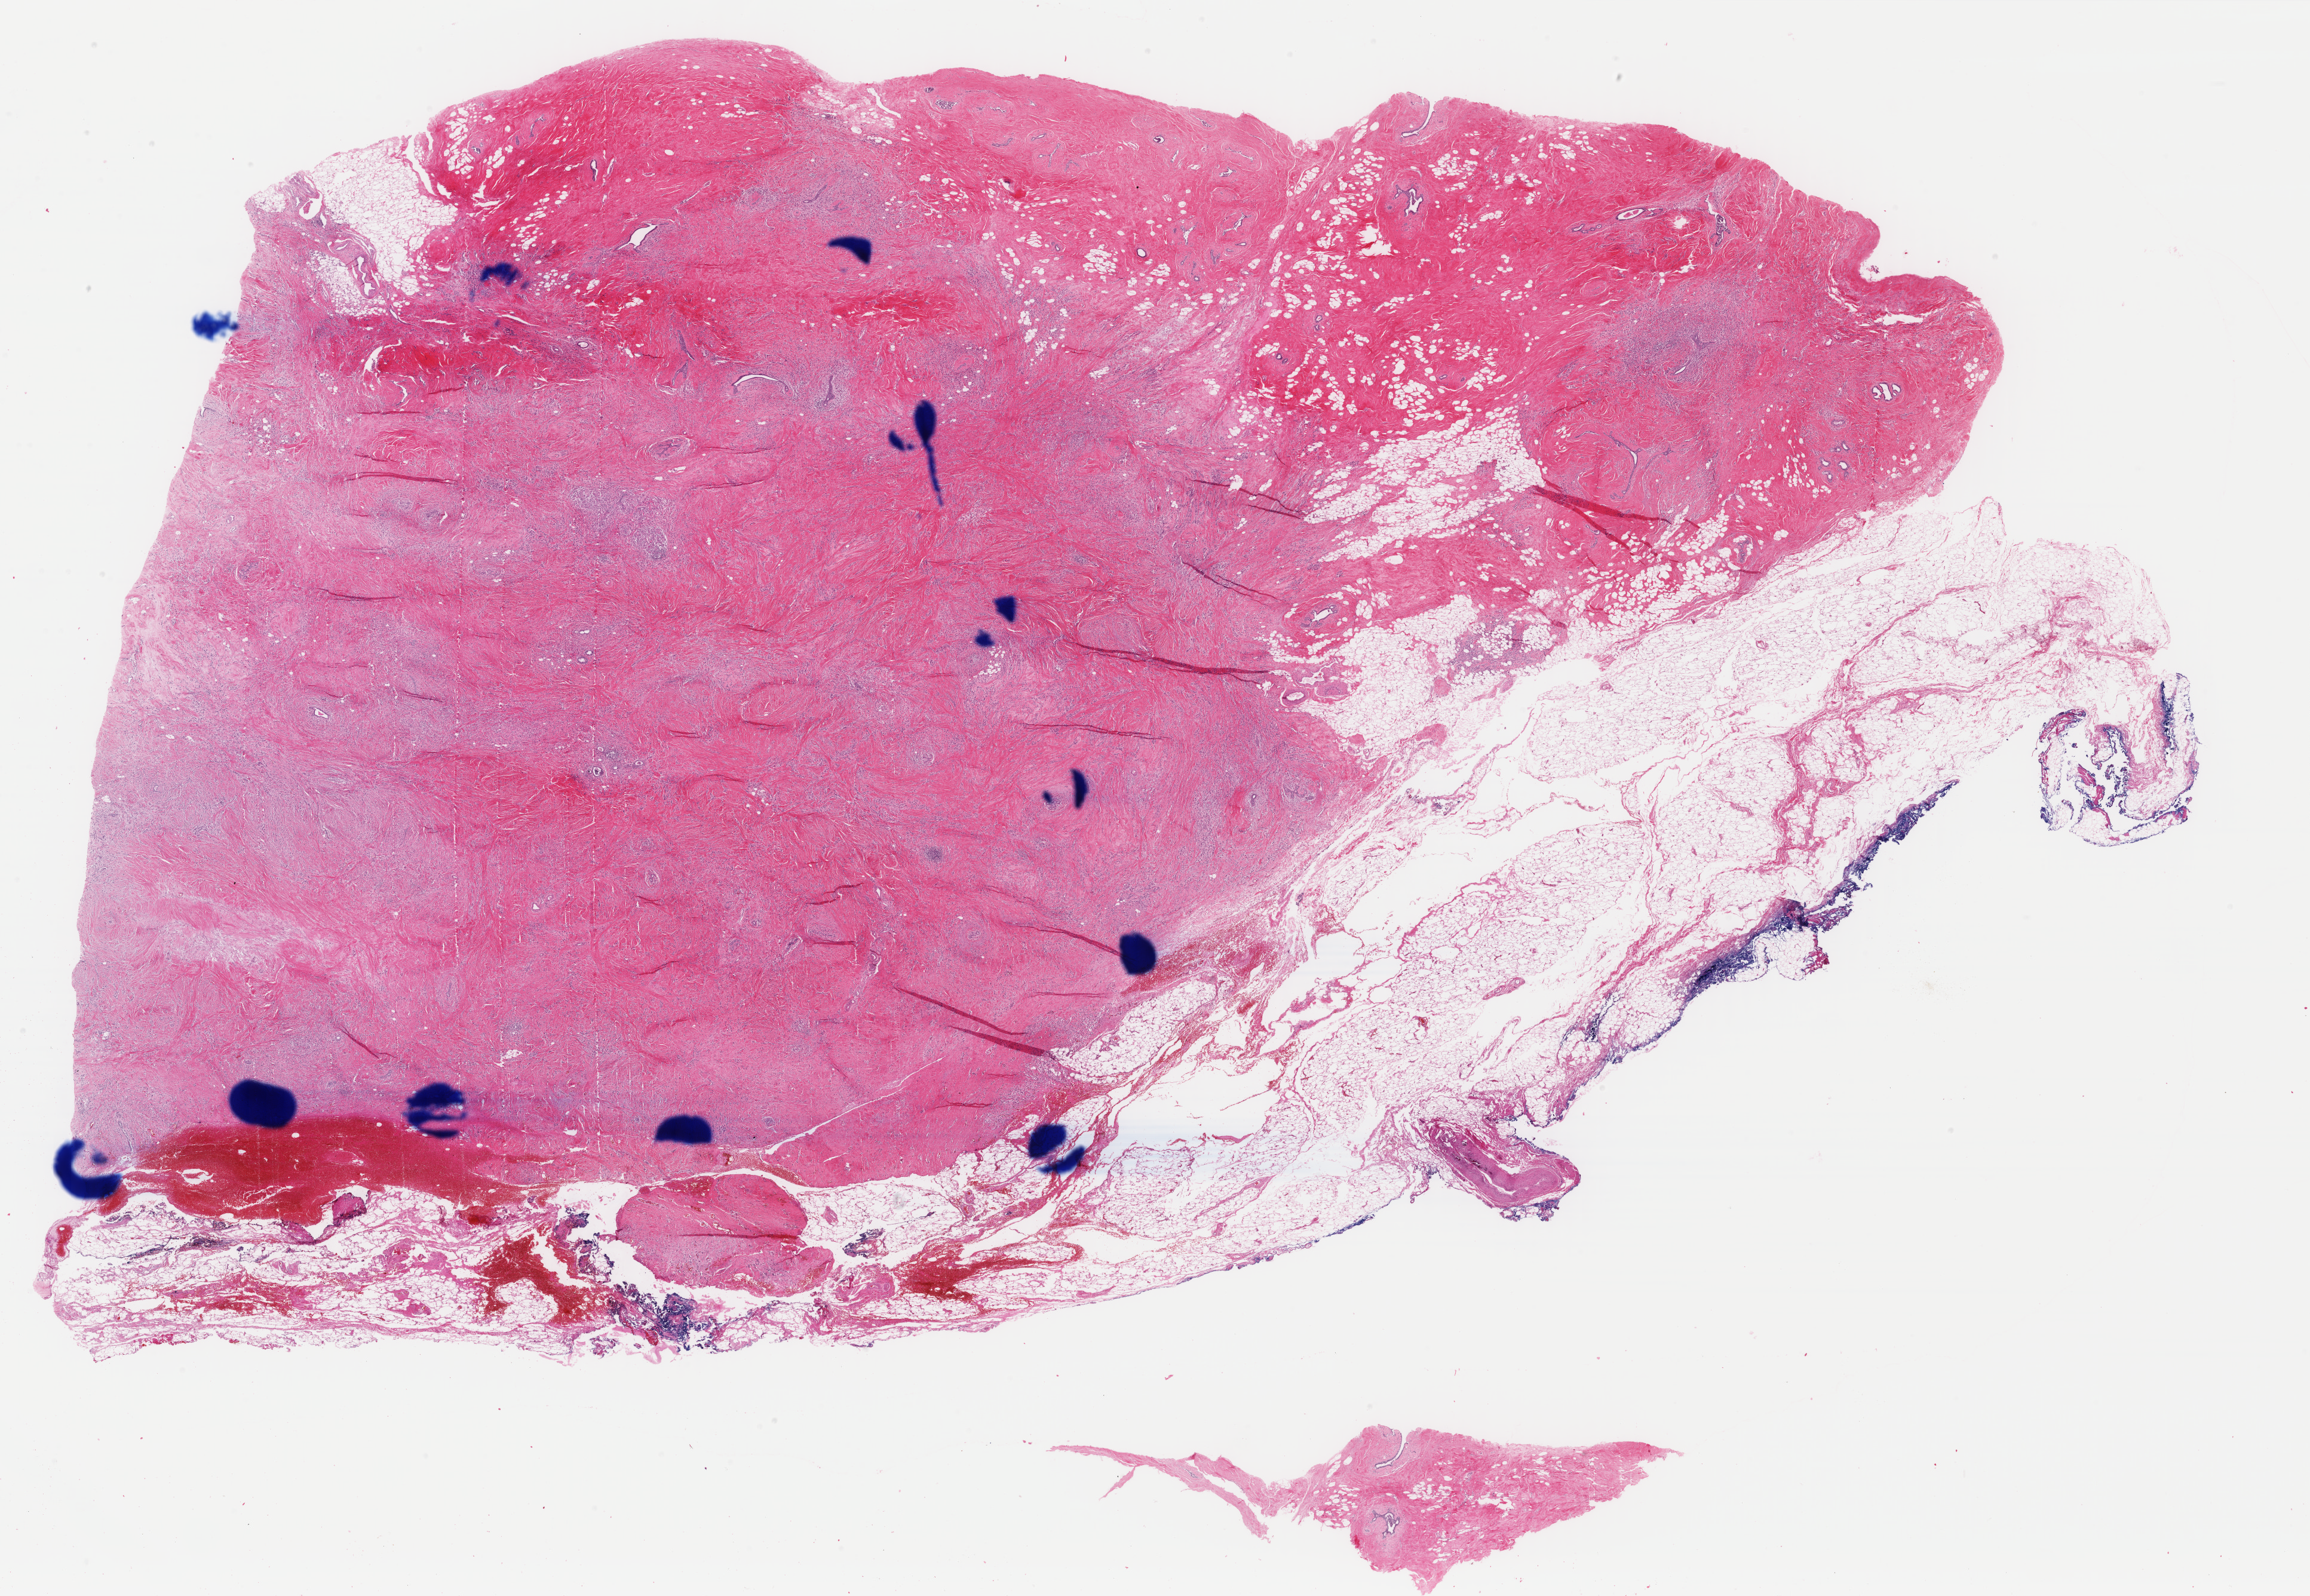
Whole-slide histology image, H&E-stained, low-resolution overview of the scanned area, about 30.7 x 21.2 mm (from a 40x scan). FFPE section. Primary tumour sample from the breast. Female patient.
TNM: T3 N1b M0. Histologic diagnosis: Lobular carcinoma, NOS. AJCC pathologic stage: IIIA (4th edition).